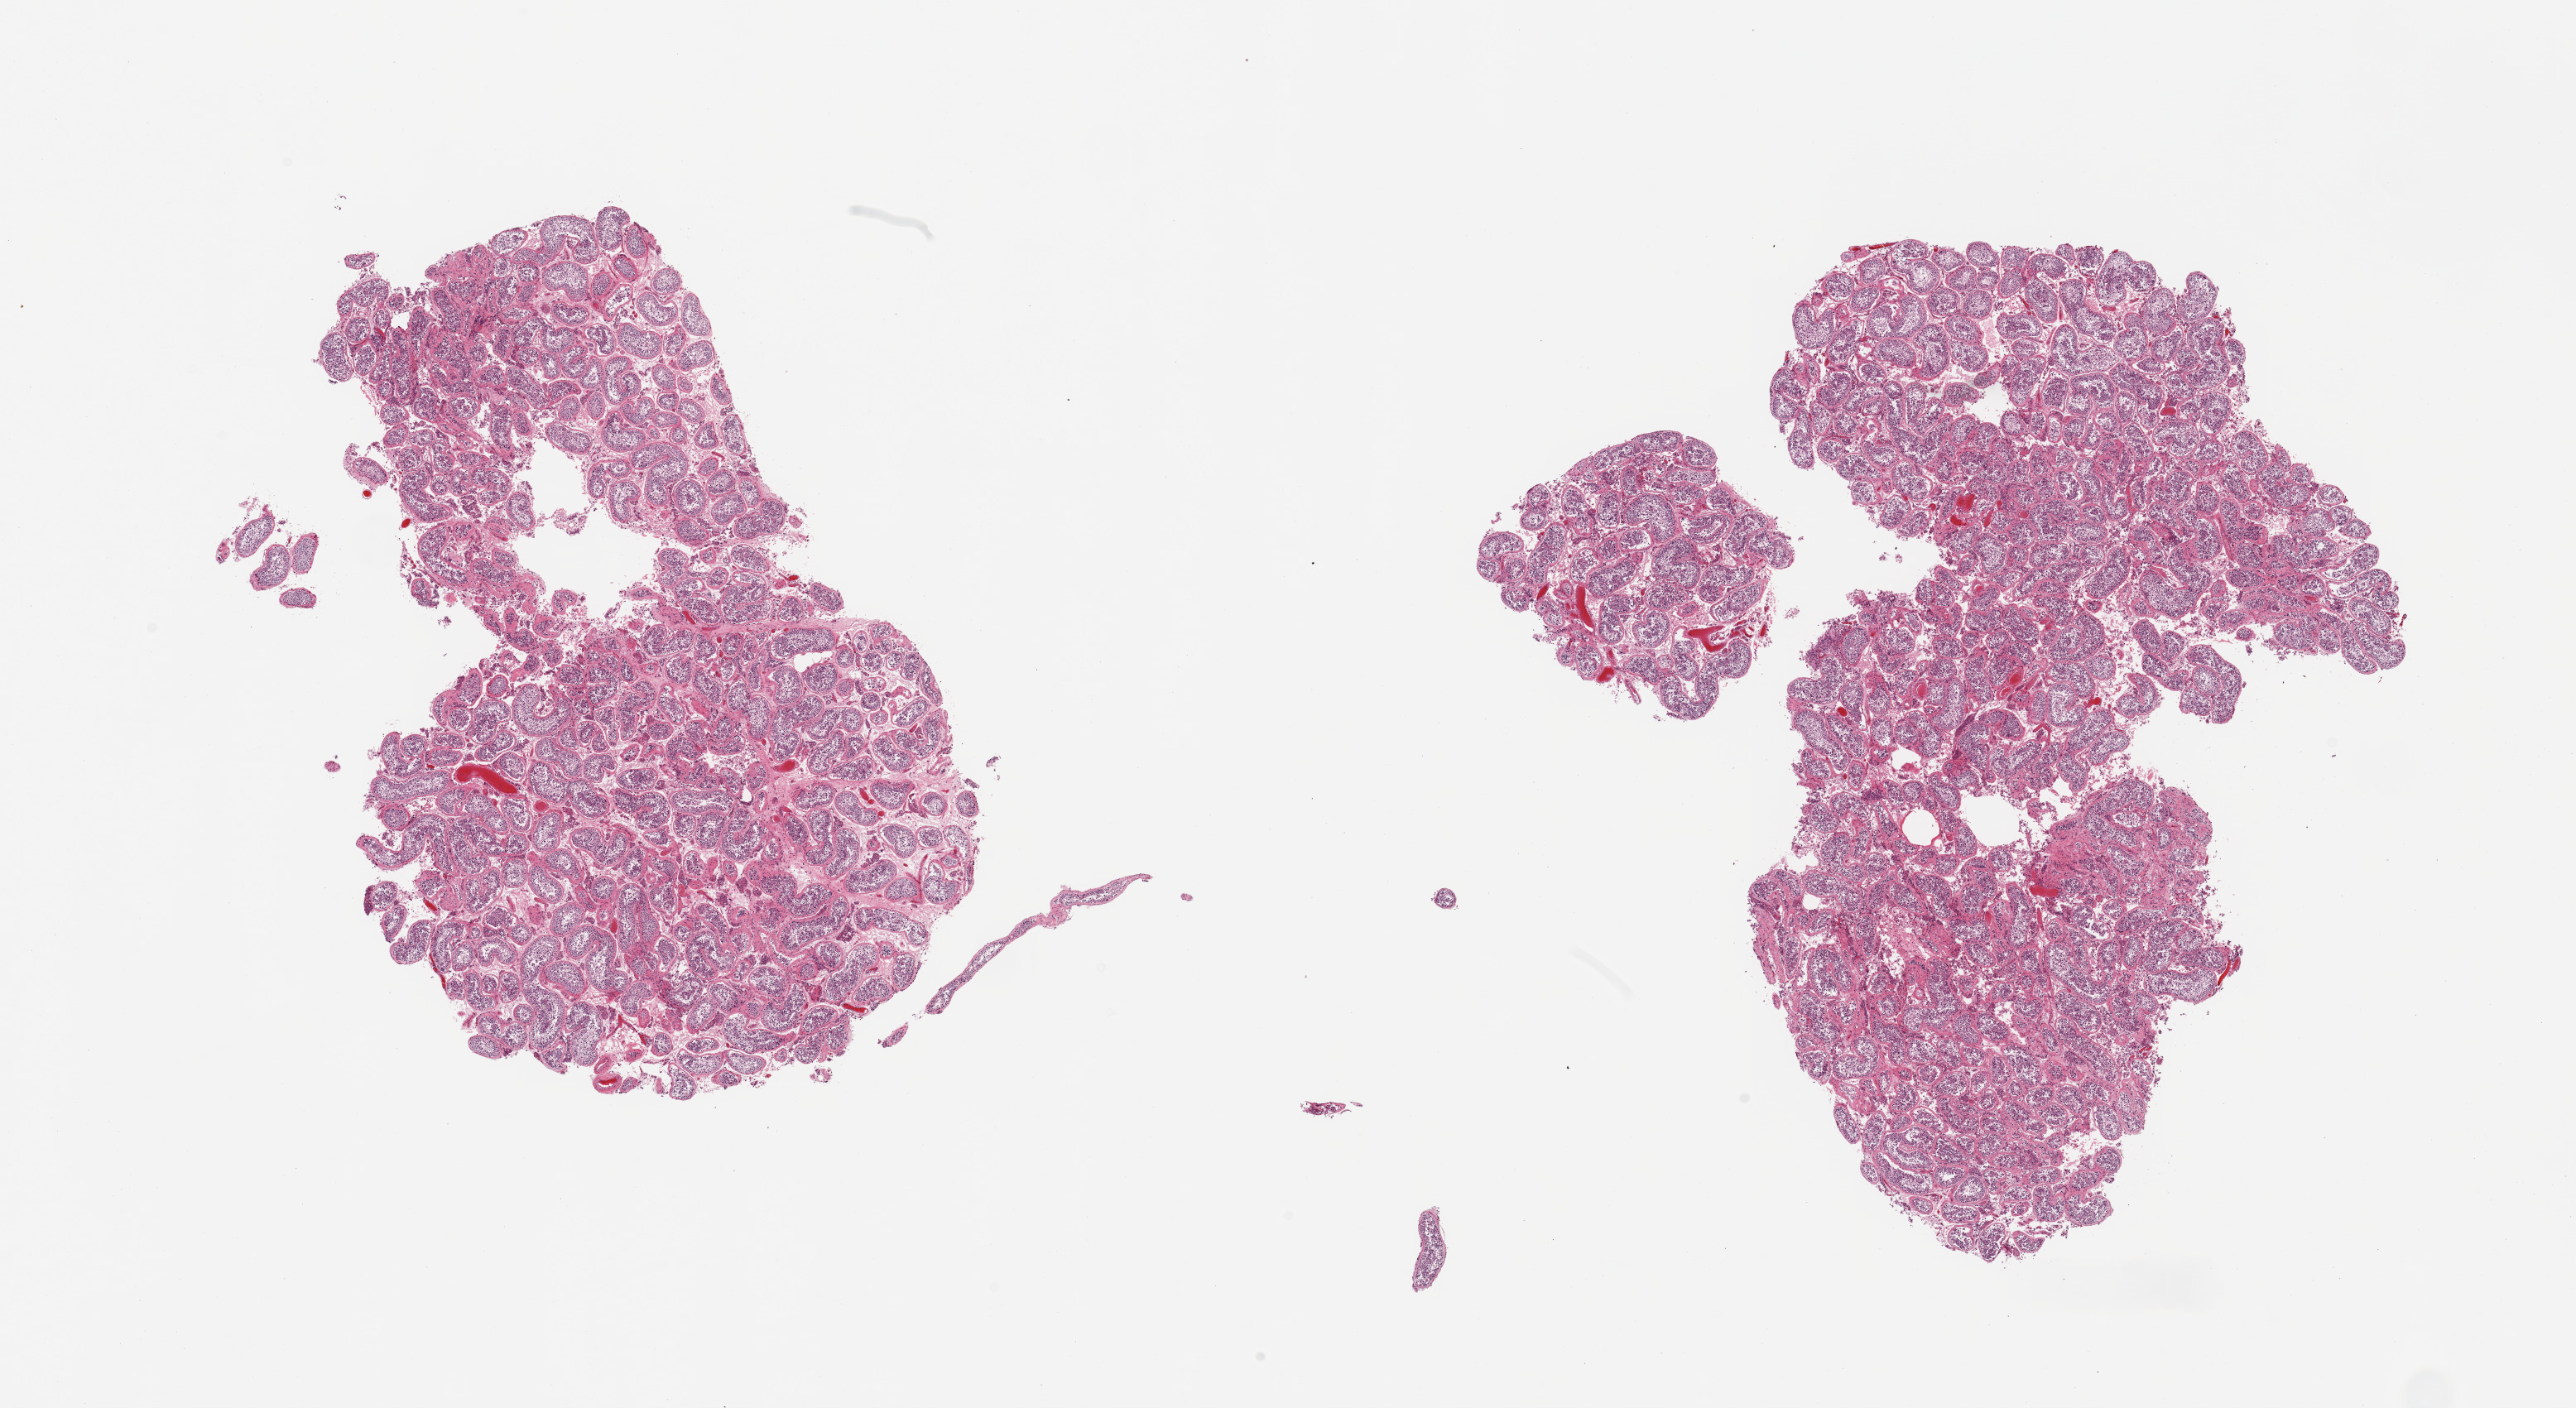
Digitized haematoxylin and eosin-stained section, shown as a low-resolution overview of the whole scanned area (about 24.6 x 13.5 mm, slide scanned at 20x), PAXgene-fixed, paraffin-embedded tissue, target tissue: testis, tissue donor sample. Donor: male.
Reviewer comment on this tissue sample: 2 pieces; spermatogenesis.